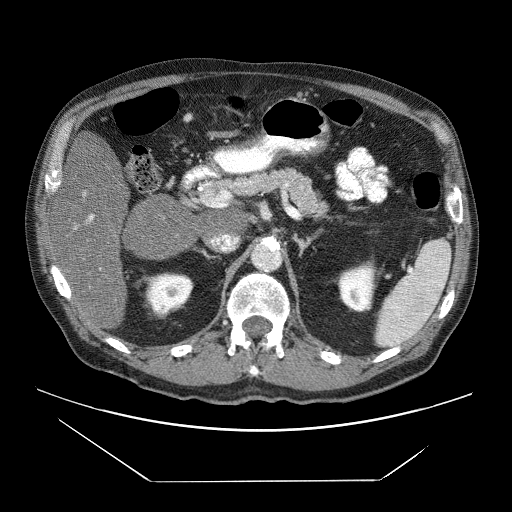
Contrast-enhanced abdominal CT (liver protocol), one axial slice. Slice 29 of 83 in the series (ordered by position). Reconstruction kernel STANDARD. 120 kVp. Soft-tissue window (W 400 / L 40 HU). 2.5 mm slice thickness. 512 × 512 image matrix, field of view 420 × 420 mm. Case-level facts recorded for this patient, not image findings: diagnosis: hepatocellular carcinoma (patient treated with transarterial chemoembolisation; whether this scan precedes or follows treatment is not stated here); TNM stage (as recorded): Stage-IVB; Child-Pugh class: B; tumour differentiation: poorly differentiated.
Outlined on this slice (semi-automatically segmented with operator editing):
- liver parenchyma outside the tumour (the mass and vessels are separate outlines, so this box may not span the whole liver): bounding box (x1, y1, x2, y2) in pixels: (52, 150, 128, 330)
- liver vessels: (74, 192, 94, 230)